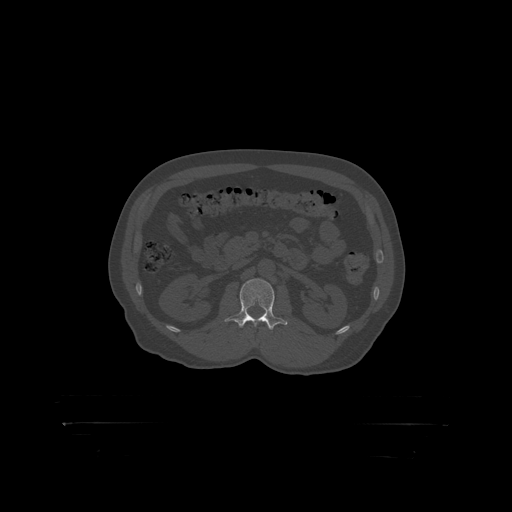
CT including the spine, one axial slice. Slice 300 of 399 in the series (ordered by position). Reconstruction kernel STANDARD. Bone window (W 1800 / L 400 HU). 512 × 512 image matrix, field of view 650 × 650 mm. Male patient, age 46 years. From the clinical record (not read from this slice): primary cancer: skin.
Structures marked on this image (semi-automatic segmentation, software-assisted and operator-edited):
- L2 vertebra: box from (x=237, y=279) to (x=275, y=319) px